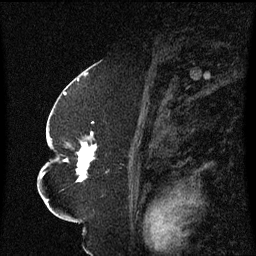
Breast MRI (dynamic contrast-enhanced), one sagittal slice; slice 37 of 60 in the series (ordered by position); dynamic contrast-enhanced series, image 2 of 3 at this slice position (ordered by acquisition); 1.5 T; TE 4.2 ms, TR 8.4 ms; 2.3 mm slice thickness; 256 × 256 image matrix. Patient: female, 52 years. Case-level facts recorded for this patient, not image findings: setting: breast cancer imaged before/during neoadjuvant chemotherapy; receptor status: HR-positive, HER2-negative.
Annotated regions visible in this slice (semi-automatic segmentation, software-assisted and operator-edited):
- analysis volume of interest (the breast-tissue region the enhancement analysis was run in; not a lesion): bounding box (x1, y1, x2, y2) in pixels: (49, 124, 122, 183)
- tumour enhancement mask (voxels above the 70 % enhancement threshold inside the analysis volume of interest): (65, 132, 97, 183)